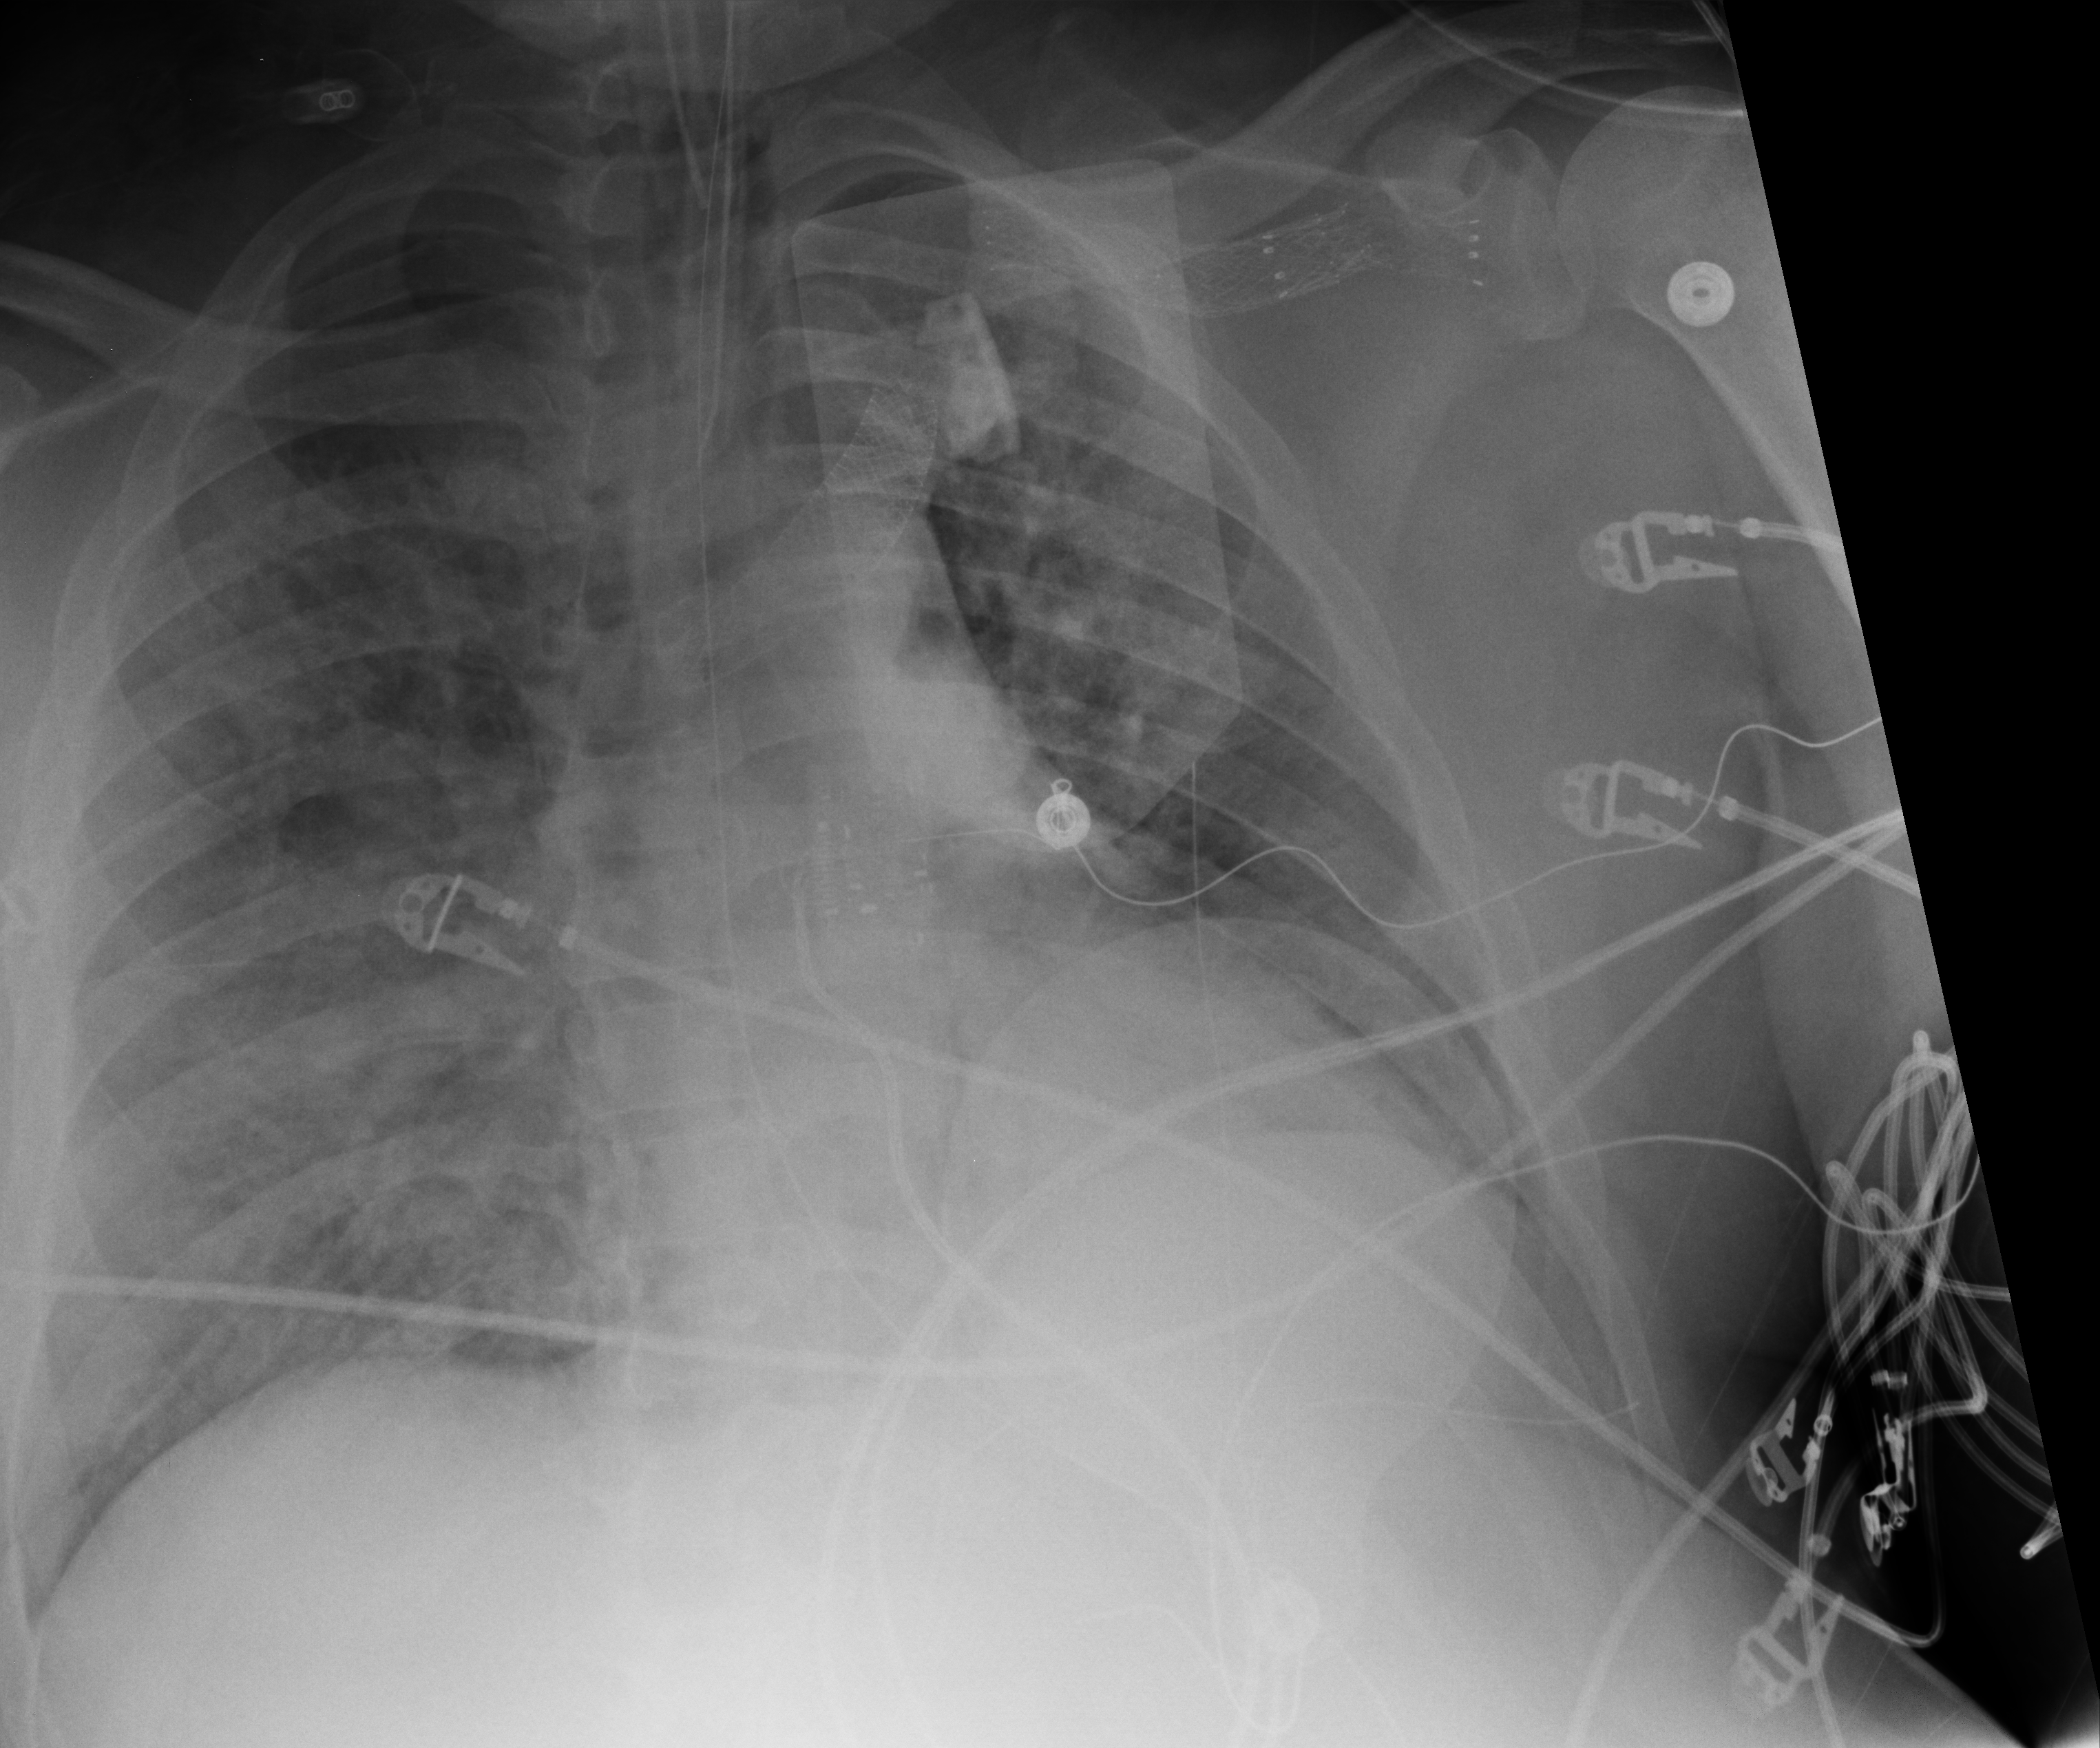
Bedside chest radiograph (computed radiography), anteroposterior (AP) projection. Patient hospitalised with COVID-19; male, aged 18–59 years.
From the hospital-stay record, not from the radiograph (when in the stay this image was taken is not recorded): admitted to intensive care during this hospital stay: yes.